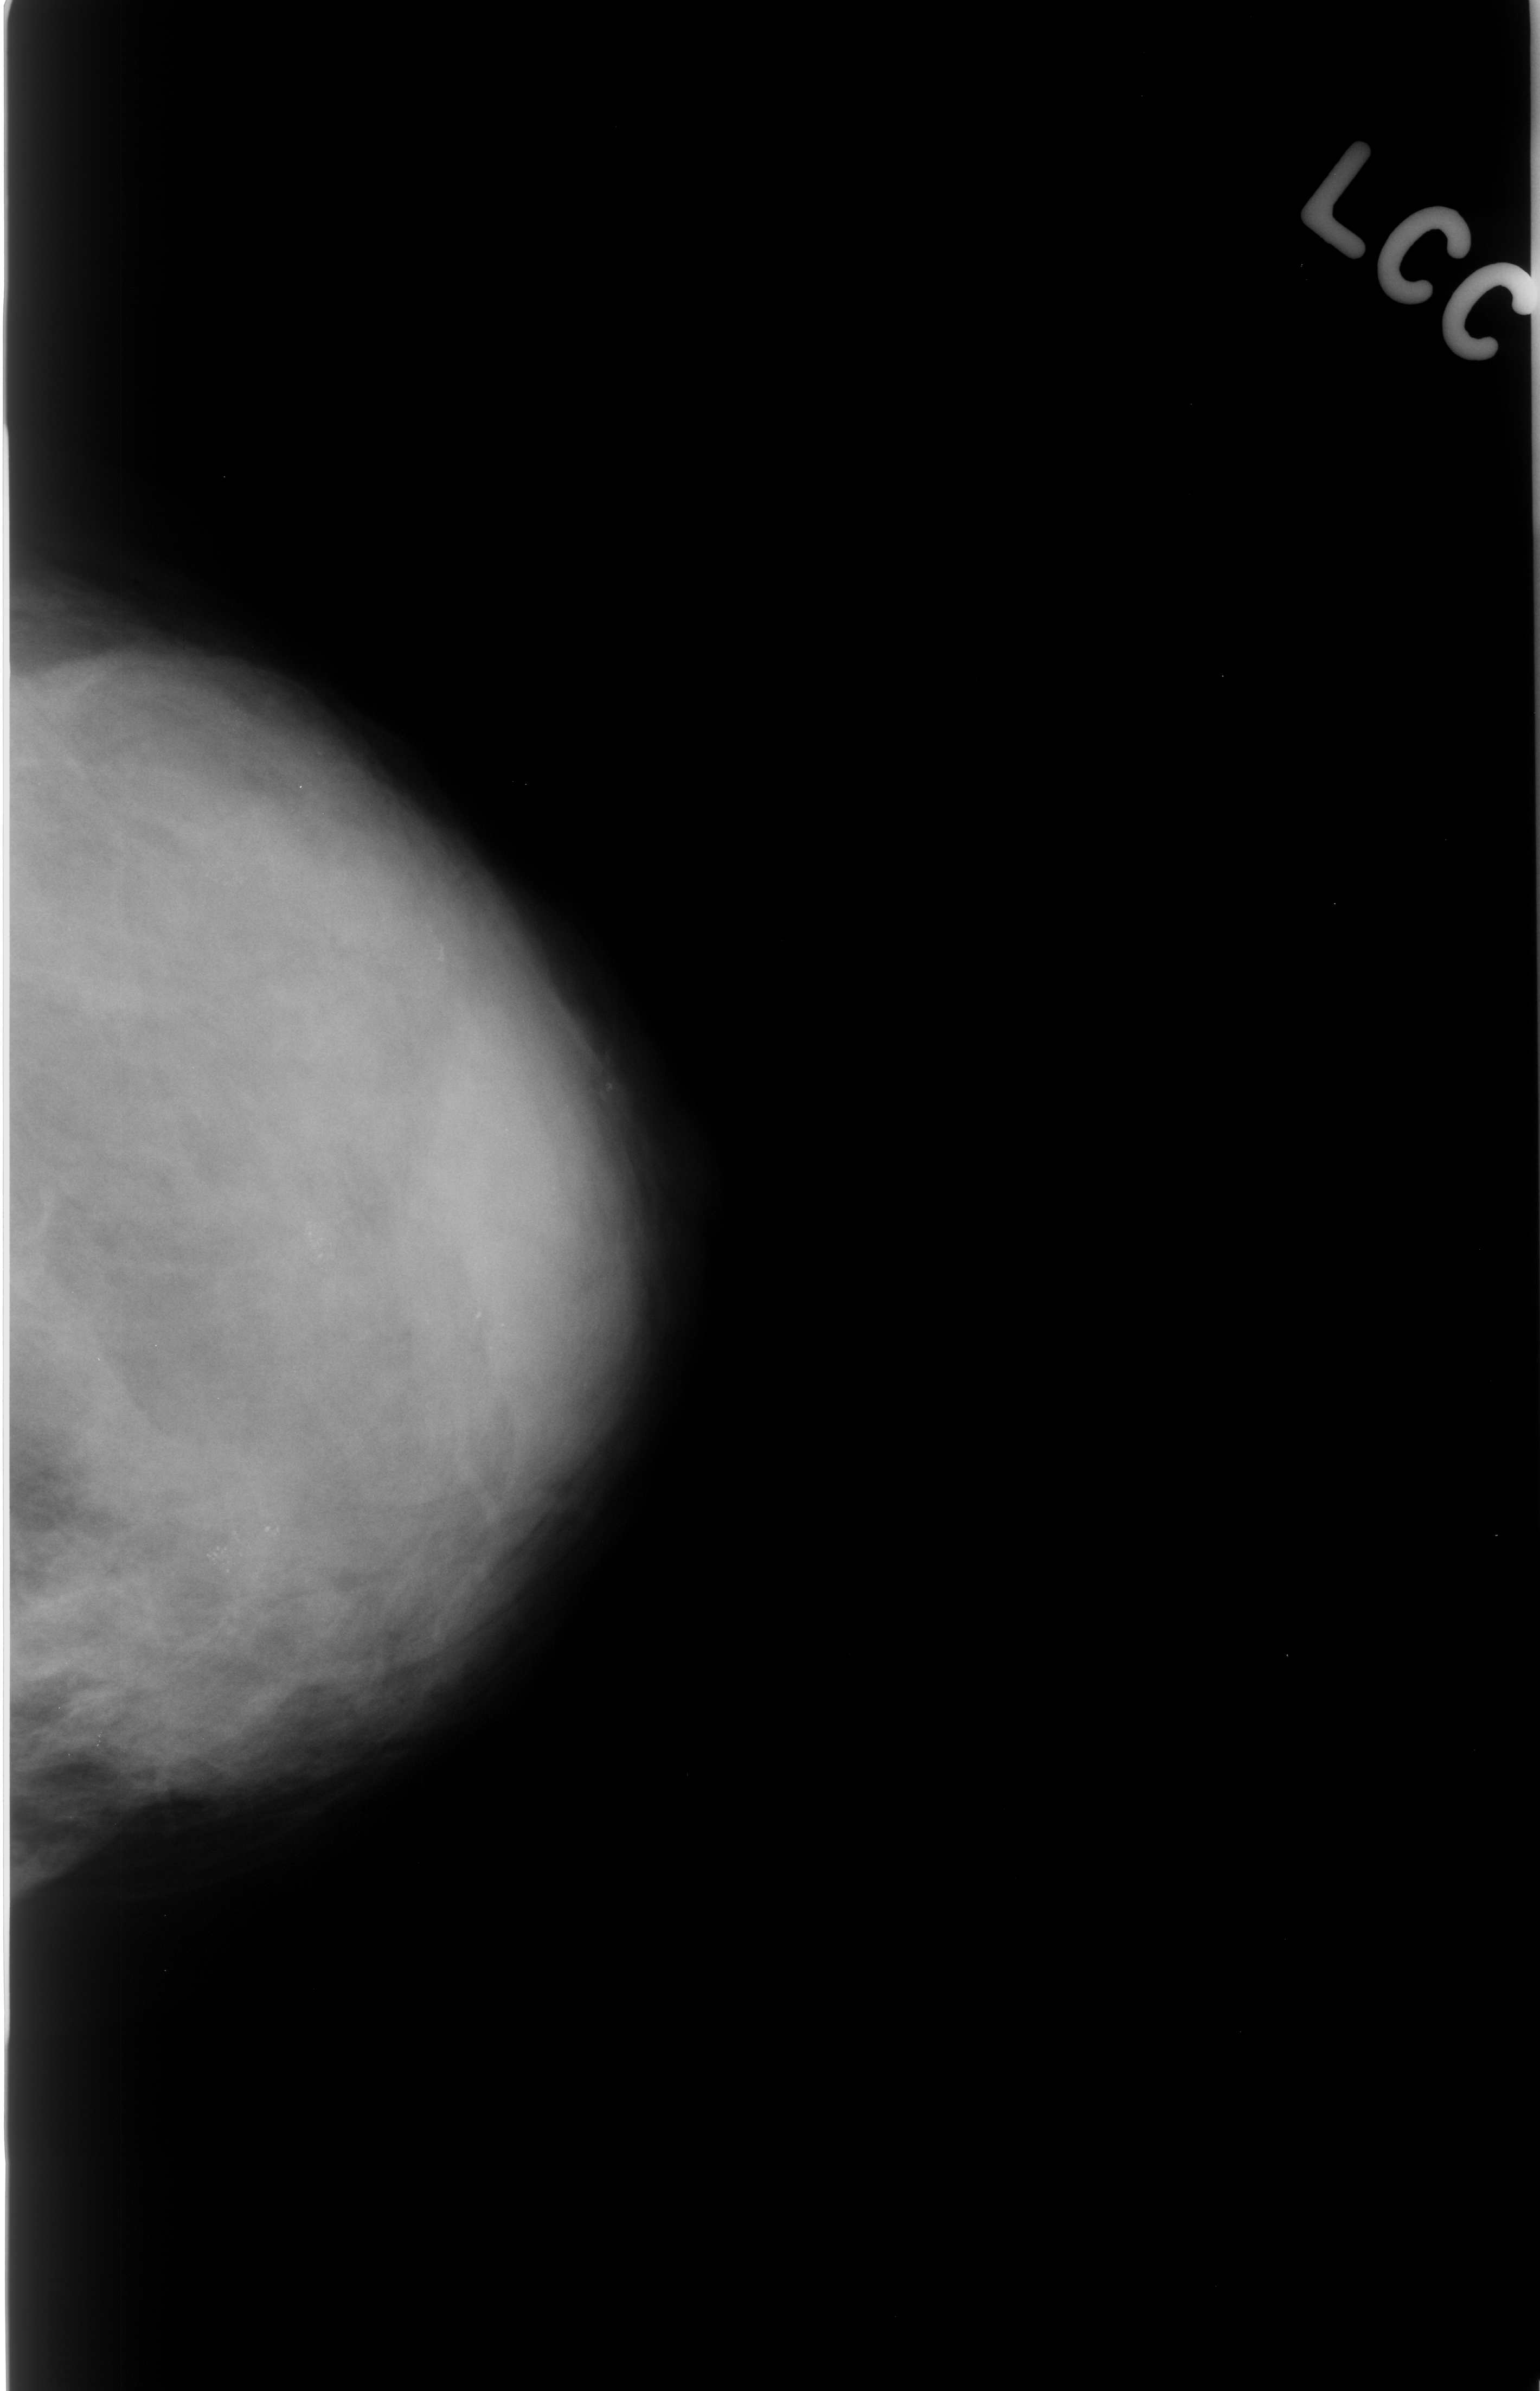
Digitized screen-film mammogram. Left breast. Craniocaudal (CC) view. BI-RADS breast density category 4 (scale 1–4). 1540 × 2391 image matrix.
Marked abnormalities (boxes around the expert regions of interest):
- Finding 1 of 2: calcifications, morphology pleomorphic, distribution clustered; BI-RADS assessment category 4; subtlety rating 4 on a 1 (subtle) to 5 (obvious) scale; pathology result (as recorded, not read from the image): benign: bounding box <73,1449,365,1741> (left, top, right, bottom; pixels)
- Finding 2 of 2: calcifications, morphology pleomorphic, distribution clustered; BI-RADS assessment category 4; pathology (as recorded): benign: <229,1158,370,1299>